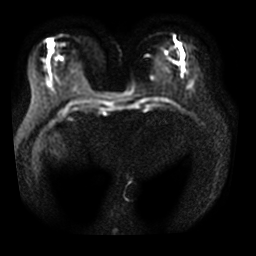
Breast MRI, one axial slice; slice 13 of 34 in the series (ordered by position); diffusion-weighted series; image 2 of 4 stored at this slice position (different b-values; order by instance number); 3 T; 5 mm slice thickness; 256 × 256 image matrix, field of view 320 × 320 mm. Female patient.
Annotated regions visible in this slice (manually delineated by an expert):
- tumour on diffusion-weighted imaging: bounding box <179,46,183,55> (left, top, right, bottom; pixels)